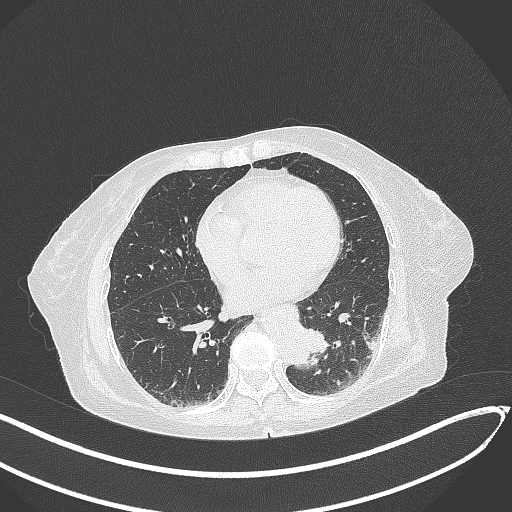
Chest CT, one axial slice; slice 87 of 324 in the series (ordered by position); reconstruction kernel B70f; 120 kVp; lung window (W 1500 / L -600 HU); 1 mm slice thickness; 512 × 512 image matrix, field of view 400 × 400 mm. Patient: female, 82 years. Case-level facts recorded for this patient, not image findings: clinical TNM (as recorded): T1b N0 M1.
Annotated regions visible in this slice (rectangle marked by the reading radiologist):
- lung tumour (recorded histology: adenocarcinoma): bounding box <298,322,334,357> (left, top, right, bottom; pixels)